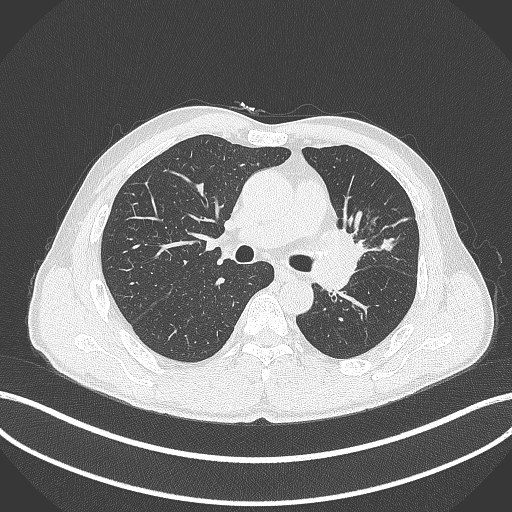
Chest CT, one axial slice; position 253 of 429 along the scan axis; reconstruction kernel B70f; lung window (W 1500 / L -600 HU); 1 mm slice thickness; 512 × 512 image matrix, field of view 400 × 400 mm. Male patient, age 57 years. Case-level facts recorded for this patient, not image findings: clinical TNM (as recorded): T2b N0 M0.
Structures marked on this image (bounding box drawn by a radiologist):
- lung tumour (recorded histology: squamous cell carcinoma): bounding box (x1, y1, x2, y2) in pixels: (317, 225, 372, 268)